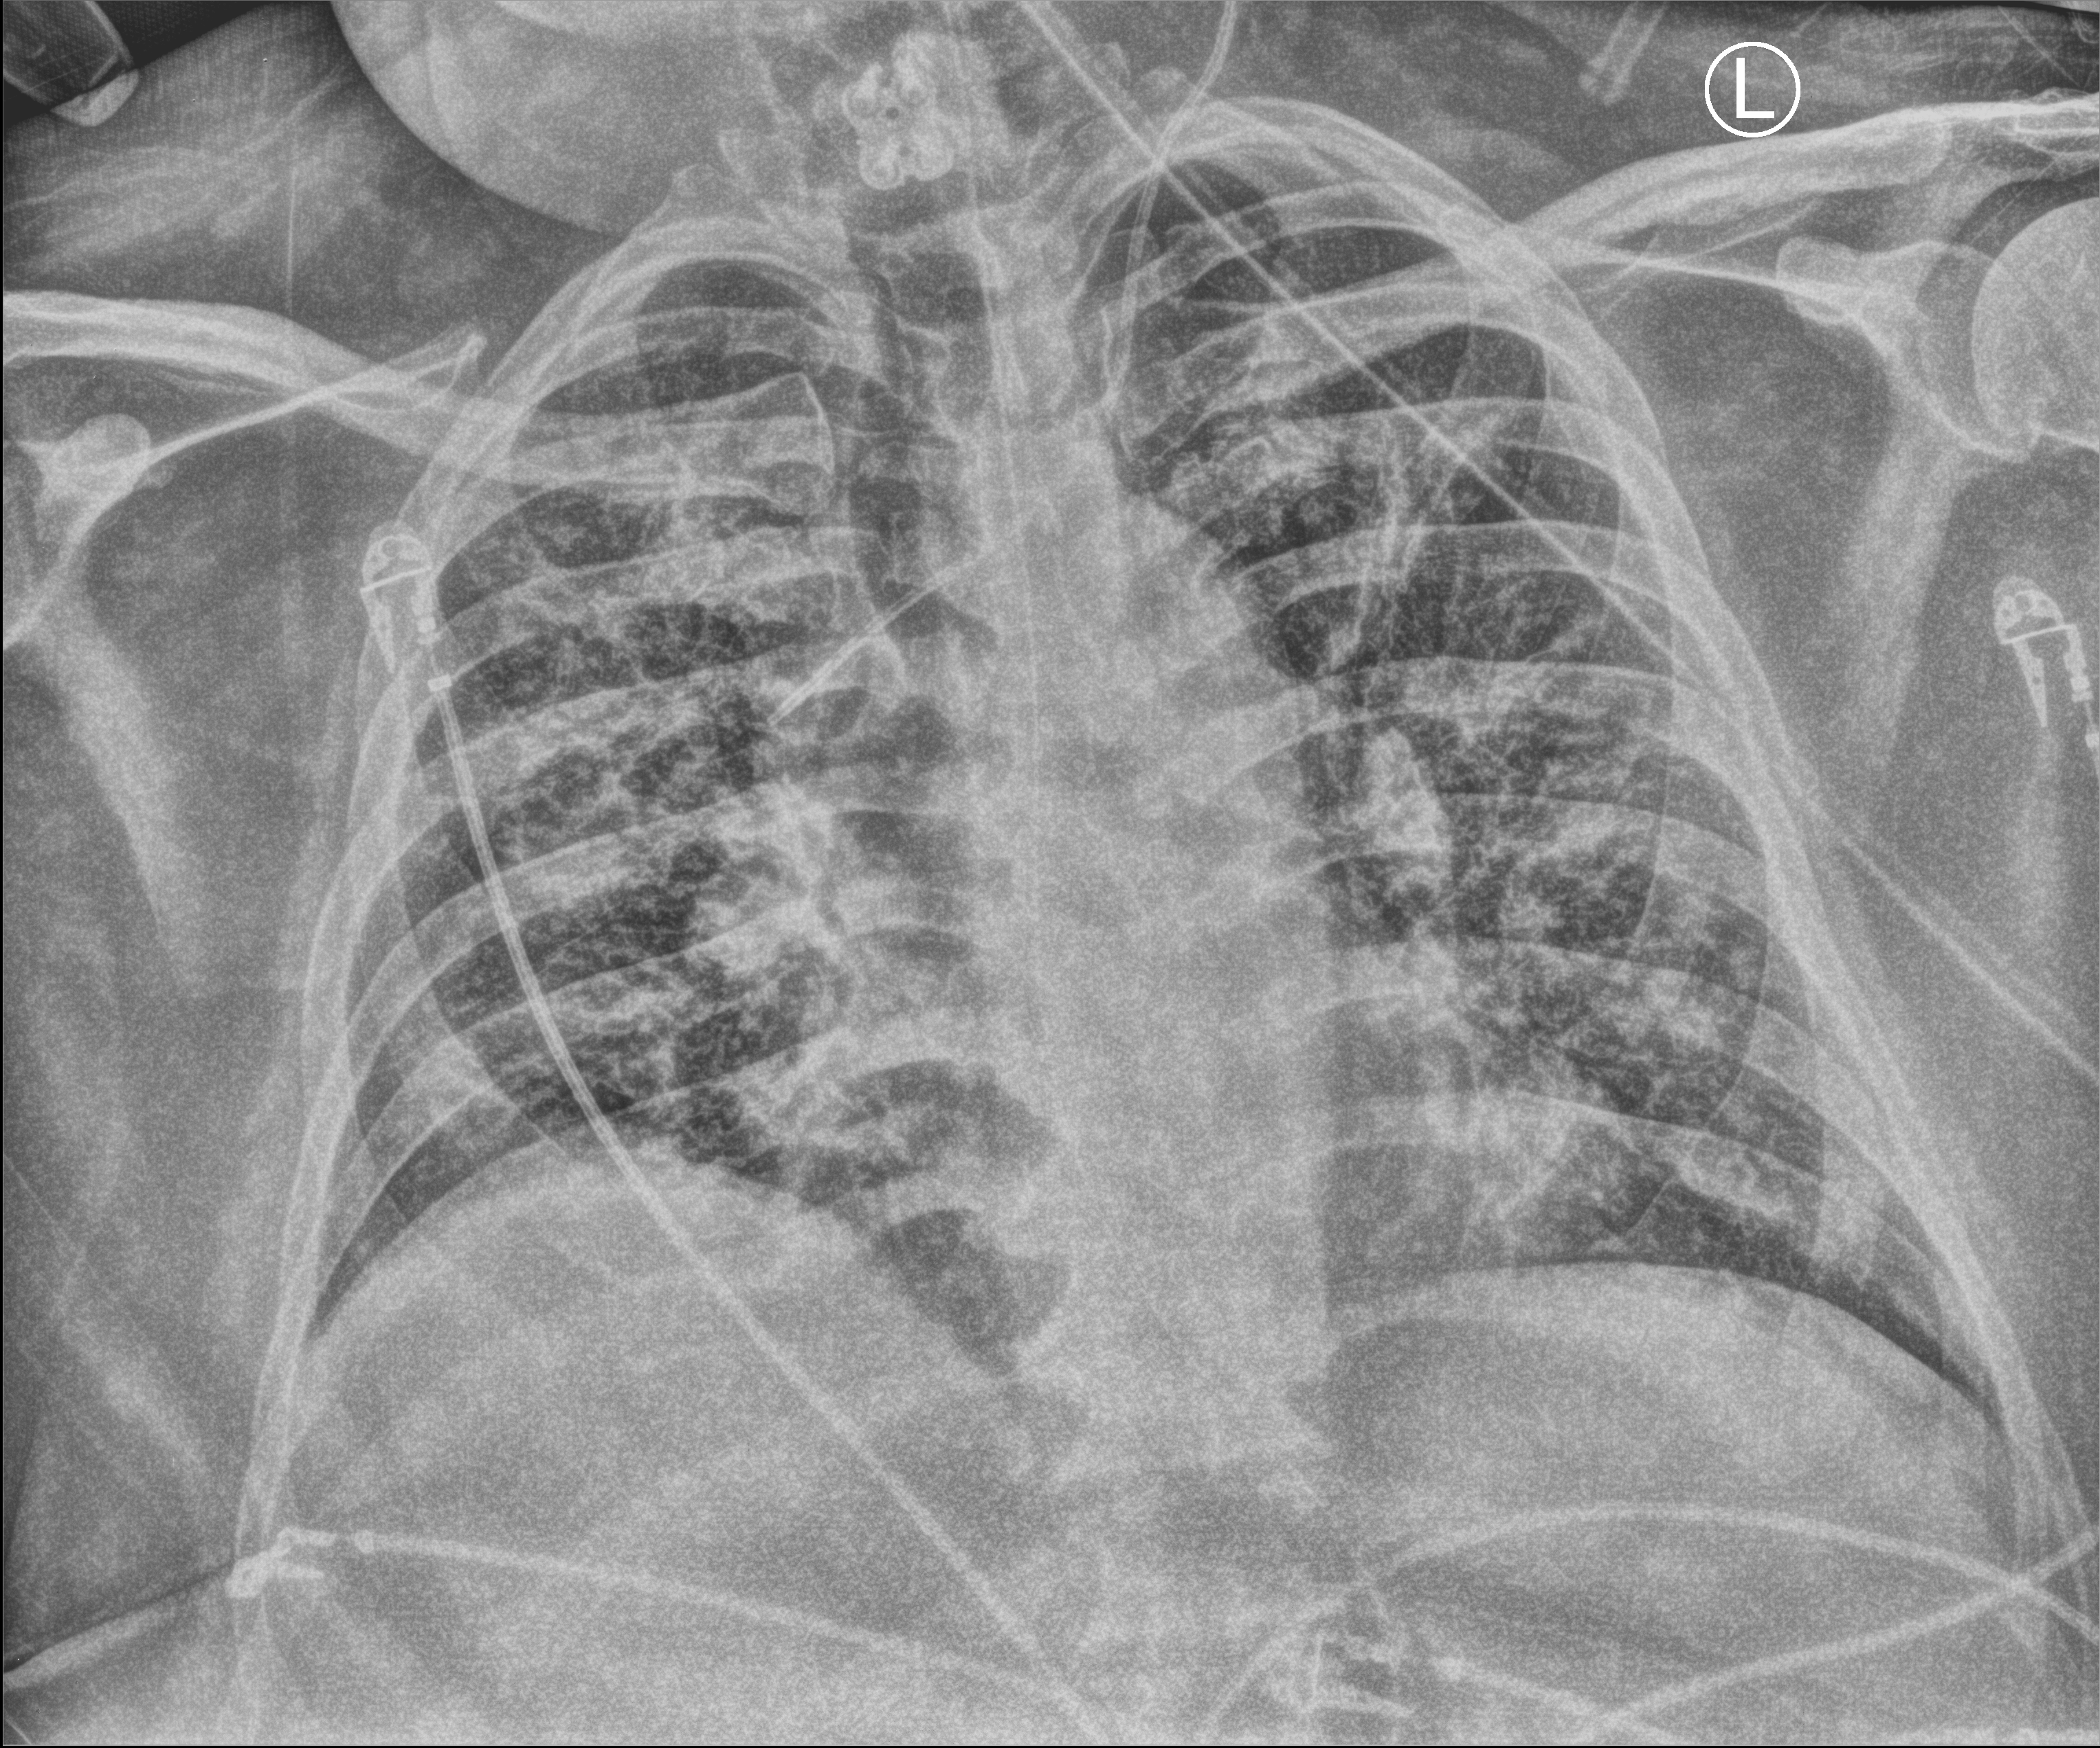
Chest X-ray (portable). Male patient hospitalised with COVID-19, age 18–59 years.
Hospital-stay facts (about this admission, not read from this image; timing relative to this image not recorded): other chronic lung disease (admission record): yes; admitted to intensive care during this hospital stay: yes; mechanically ventilated during this hospital stay: yes.